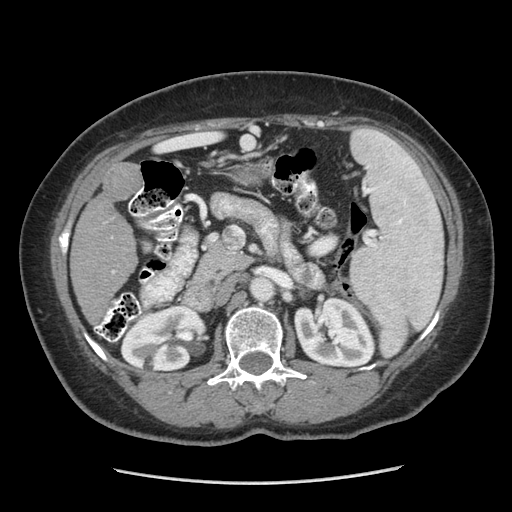
Contrast-enhanced abdominal CT (liver protocol), one axial slice; position 132 of 185 along the scan axis; reconstruction kernel STANDARD; 140 kVp; soft-tissue window (W 400 / L 40 HU); 2.5 mm slice thickness; 512 × 512 image matrix. From the clinical record (not read from this slice): diagnosis: hepatocellular carcinoma (patient treated with transarterial chemoembolisation; whether this scan precedes or follows treatment is not stated here); TNM stage (as recorded): Stage-I; Child-Pugh class: A; tumour differentiation: poorly differentiated.
Structures marked on this image (semi-automatically segmented with operator editing):
- liver parenchyma outside the tumour (the mass and vessels are separate outlines, so this box may not span the whole liver): bounding box [x1, y1, x2, y2] px = [70, 162, 140, 322]
- mass: [103, 164, 141, 200]
- liver vessels: [112, 270, 115, 273]